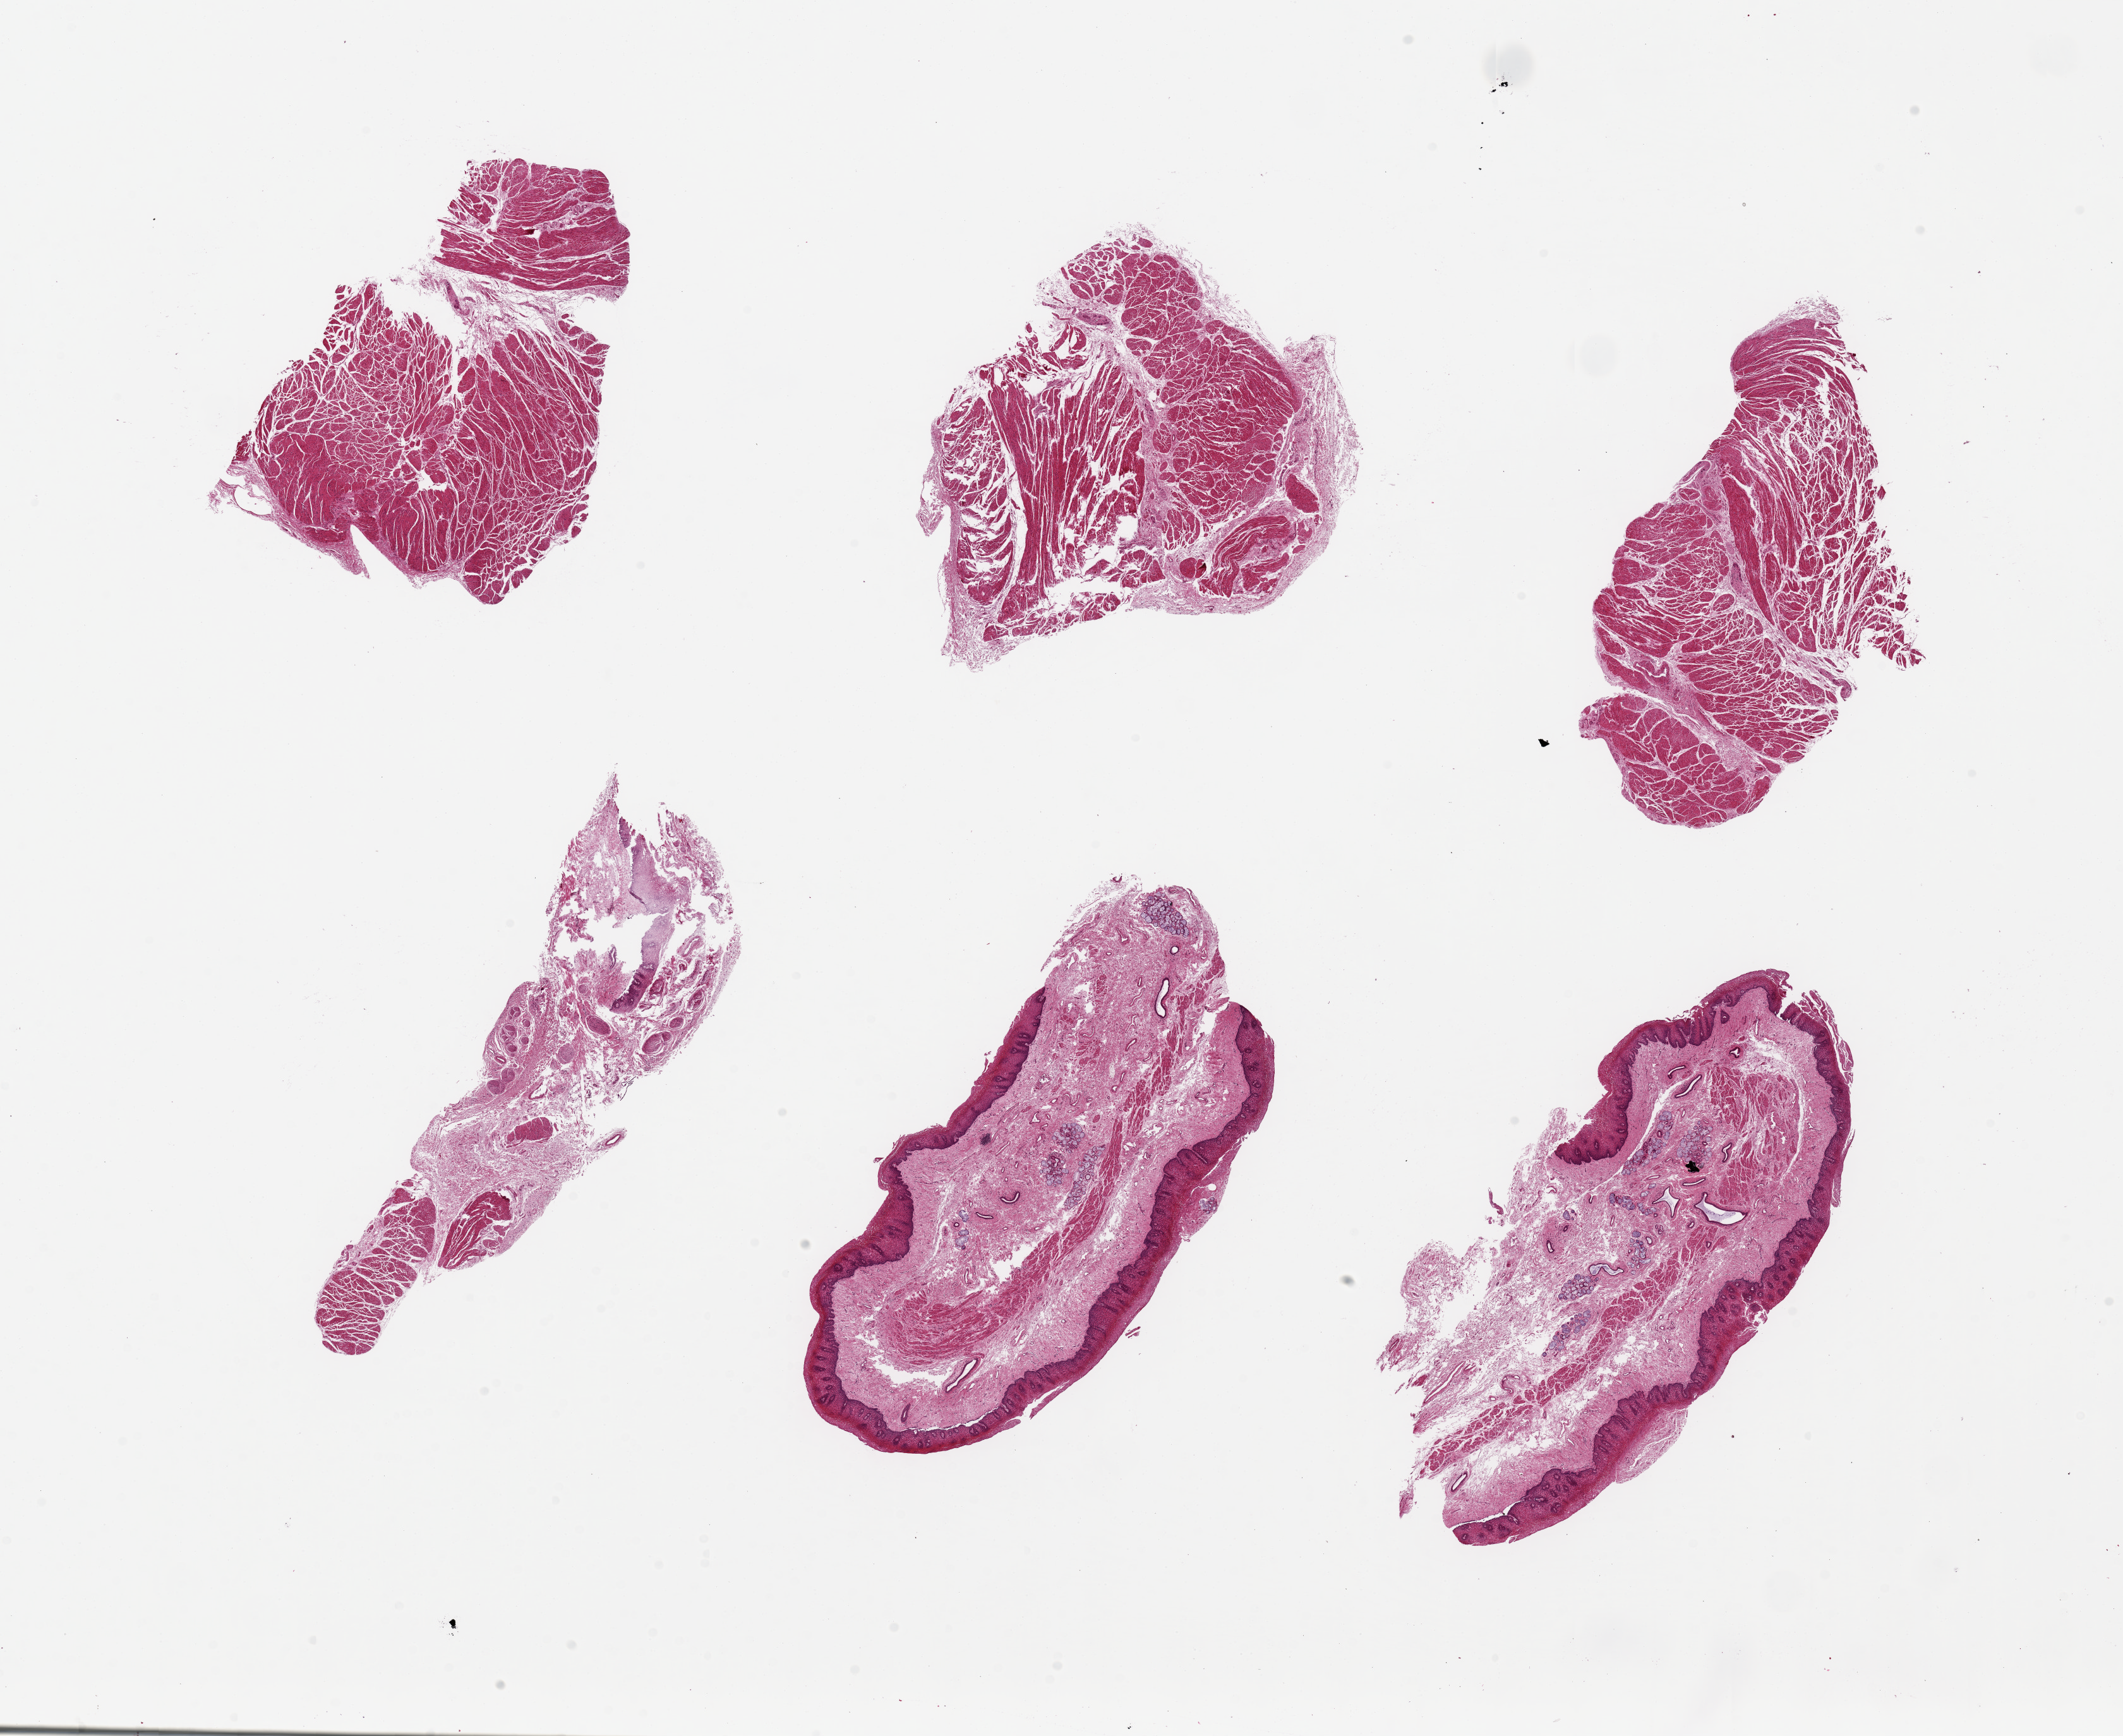
Digitized H&E-stained section — shown as a low-resolution overview of the whole scanned area (about 26.6 x 21.7 mm, from a 20x scan). PAXgene-fixed, paraffin-embedded tissue. Section of esophageal muscle (target tissue). Donor tissue sample.
Pathologist's review note for this sample: 6 pieces, up to 8x4mm; 3 muscularis only; 2 mucosa only; 1 fibromuscular tissue.